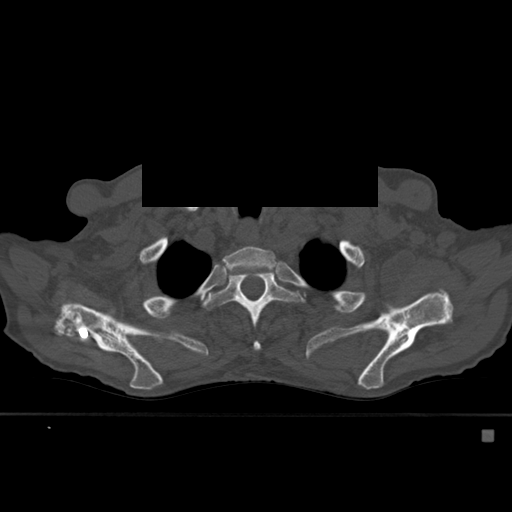
CT including the spine, one axial slice. Slice 436 of 527 in the series (ordered by position). Bone window (W 1800 / L 400 HU). 1.5 mm slice thickness. 512 × 512 image matrix, field of view 373 × 373 mm. Male patient, age 78 years. Case-level facts recorded for this patient, not image findings: primary cancer: prostate.
Annotated regions visible in this slice (semi-automatic segmentation, software-assisted and operator-edited):
- T2 vertebra: bounding box <222,246,276,279> (left, top, right, bottom; pixels)
- T3 vertebra: <204,271,296,352>